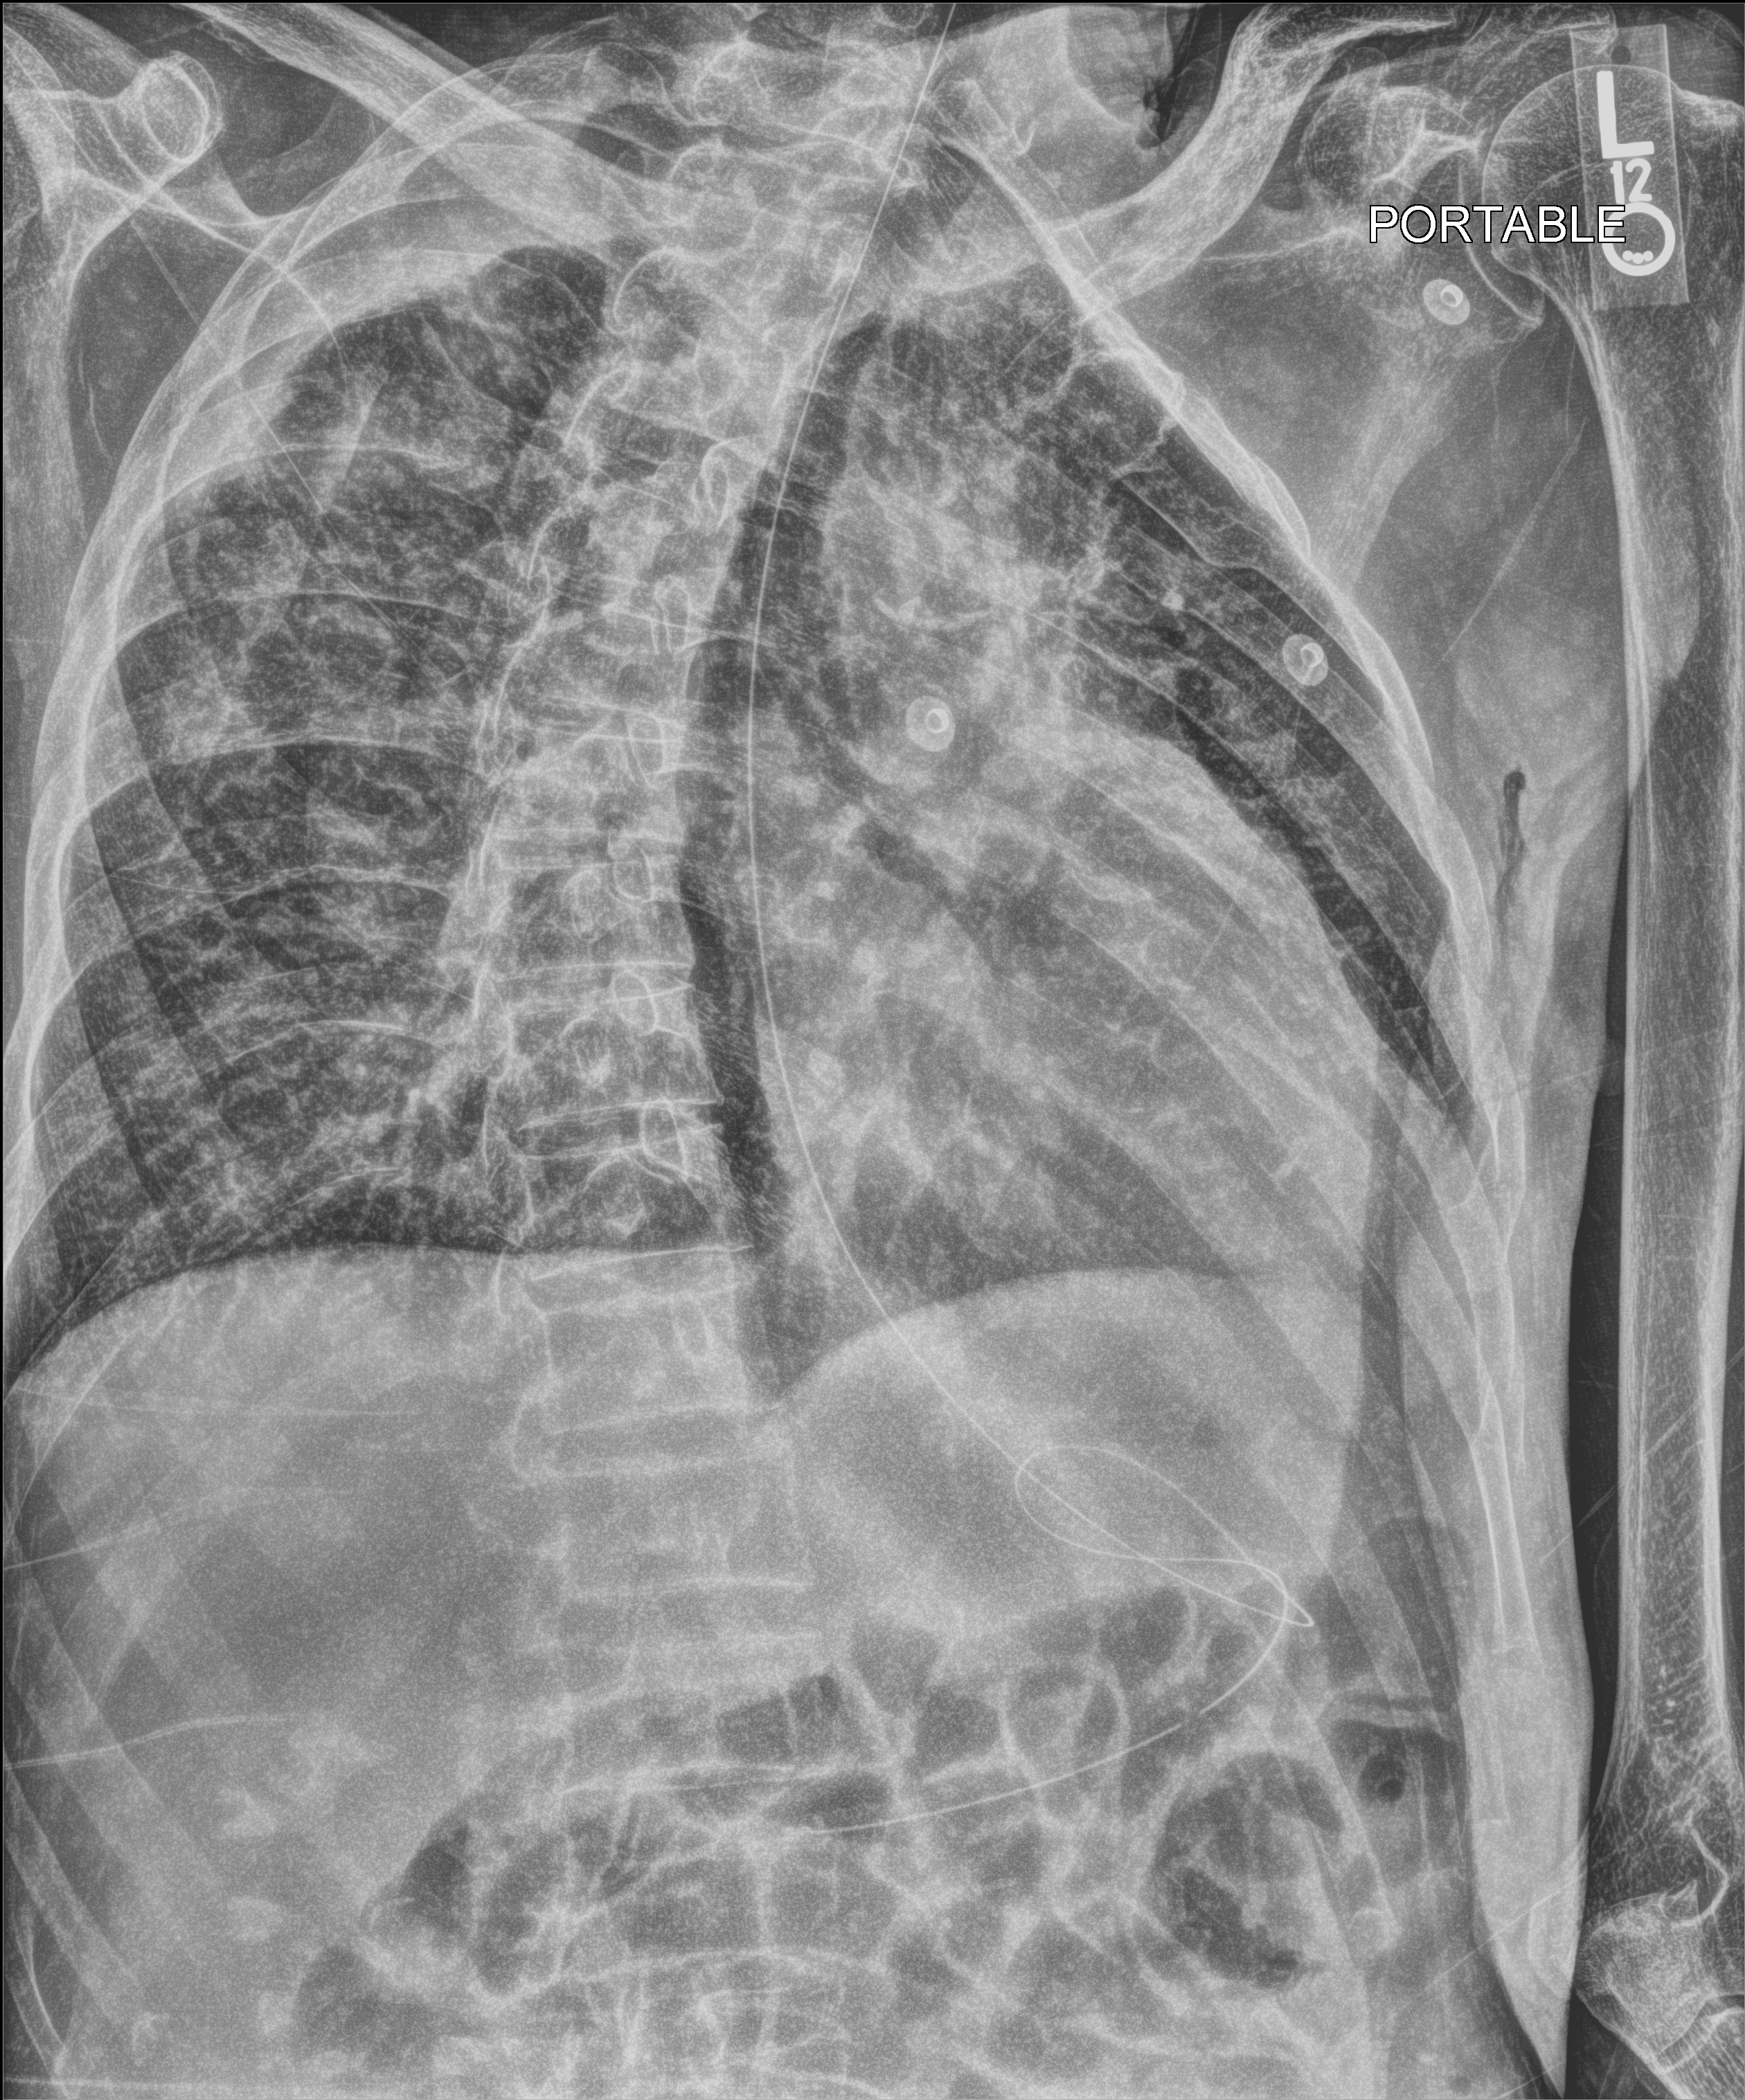
Portable chest radiograph, anteroposterior (AP) projection. Male patient hospitalised with COVID-19, age 75–90 years.
Admission-level facts for this patient (not findings on this image; timing relative to this image not recorded): admitted to intensive care during this hospital stay: no.